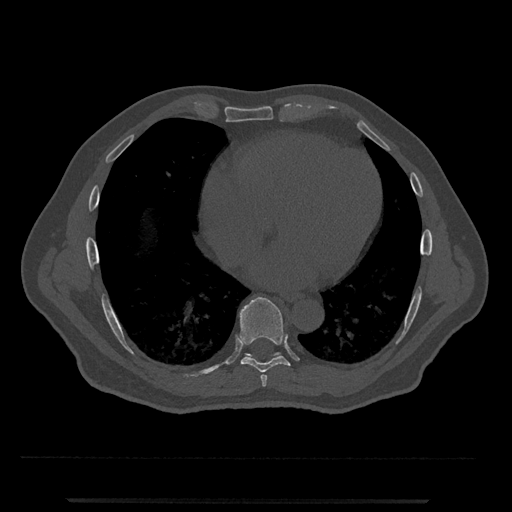
CT including the spine, one axial slice. Slice 620 of 797 in the series (ordered by position). Bone window (W 1800 / L 400 HU). 0.5 mm slice thickness. 512 × 512 image matrix, field of view 419 × 419 mm. Male patient, age 63 years. From the clinical record (not read from this slice): primary cancer: prostate.
Annotated regions visible in this slice (semi-automatic segmentation, software-assisted and operator-edited):
- T7 vertebra: bounding box (x1, y1, x2, y2) in pixels: (260, 374, 267, 387)
- T8 vertebra: (239, 296, 291, 373)
- T9 vertebra: (245, 352, 281, 358)